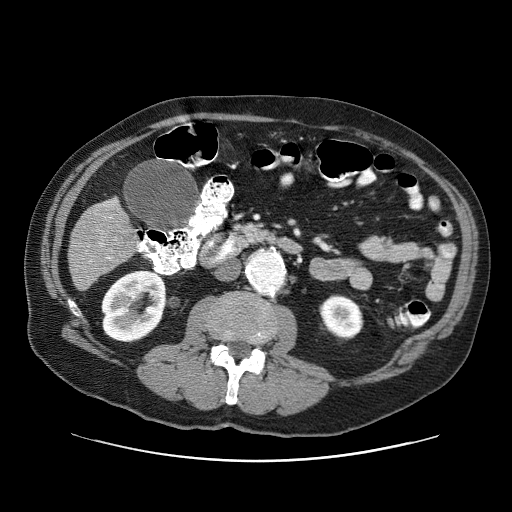
Contrast-enhanced abdominal CT (liver protocol), one axial slice. Position 12 of 87 along the scan axis. Reconstruction kernel STANDARD. 120 kVp. One of 3 acquisitions stored at this slice position. Soft-tissue window (W 400 / L 40 HU). 2.5 mm slice thickness. 512 × 512 image matrix. Case-level facts recorded for this patient, not image findings: diagnosis: hepatocellular carcinoma (patient treated with transarterial chemoembolisation; whether this scan precedes or follows treatment is not stated here); TNM stage (as recorded): Stage-IIIA; Child-Pugh class: A; tumour differentiation: well differentiated; tumour nodularity: multinodular.
Outlined on this slice (semi-automatically segmented with operator editing):
- liver parenchyma outside the tumour (the mass and vessels are separate outlines, so this box may not span the whole liver): bounding box <68,198,132,290> (left, top, right, bottom; pixels)
- liver vessels: <107,202,113,259>